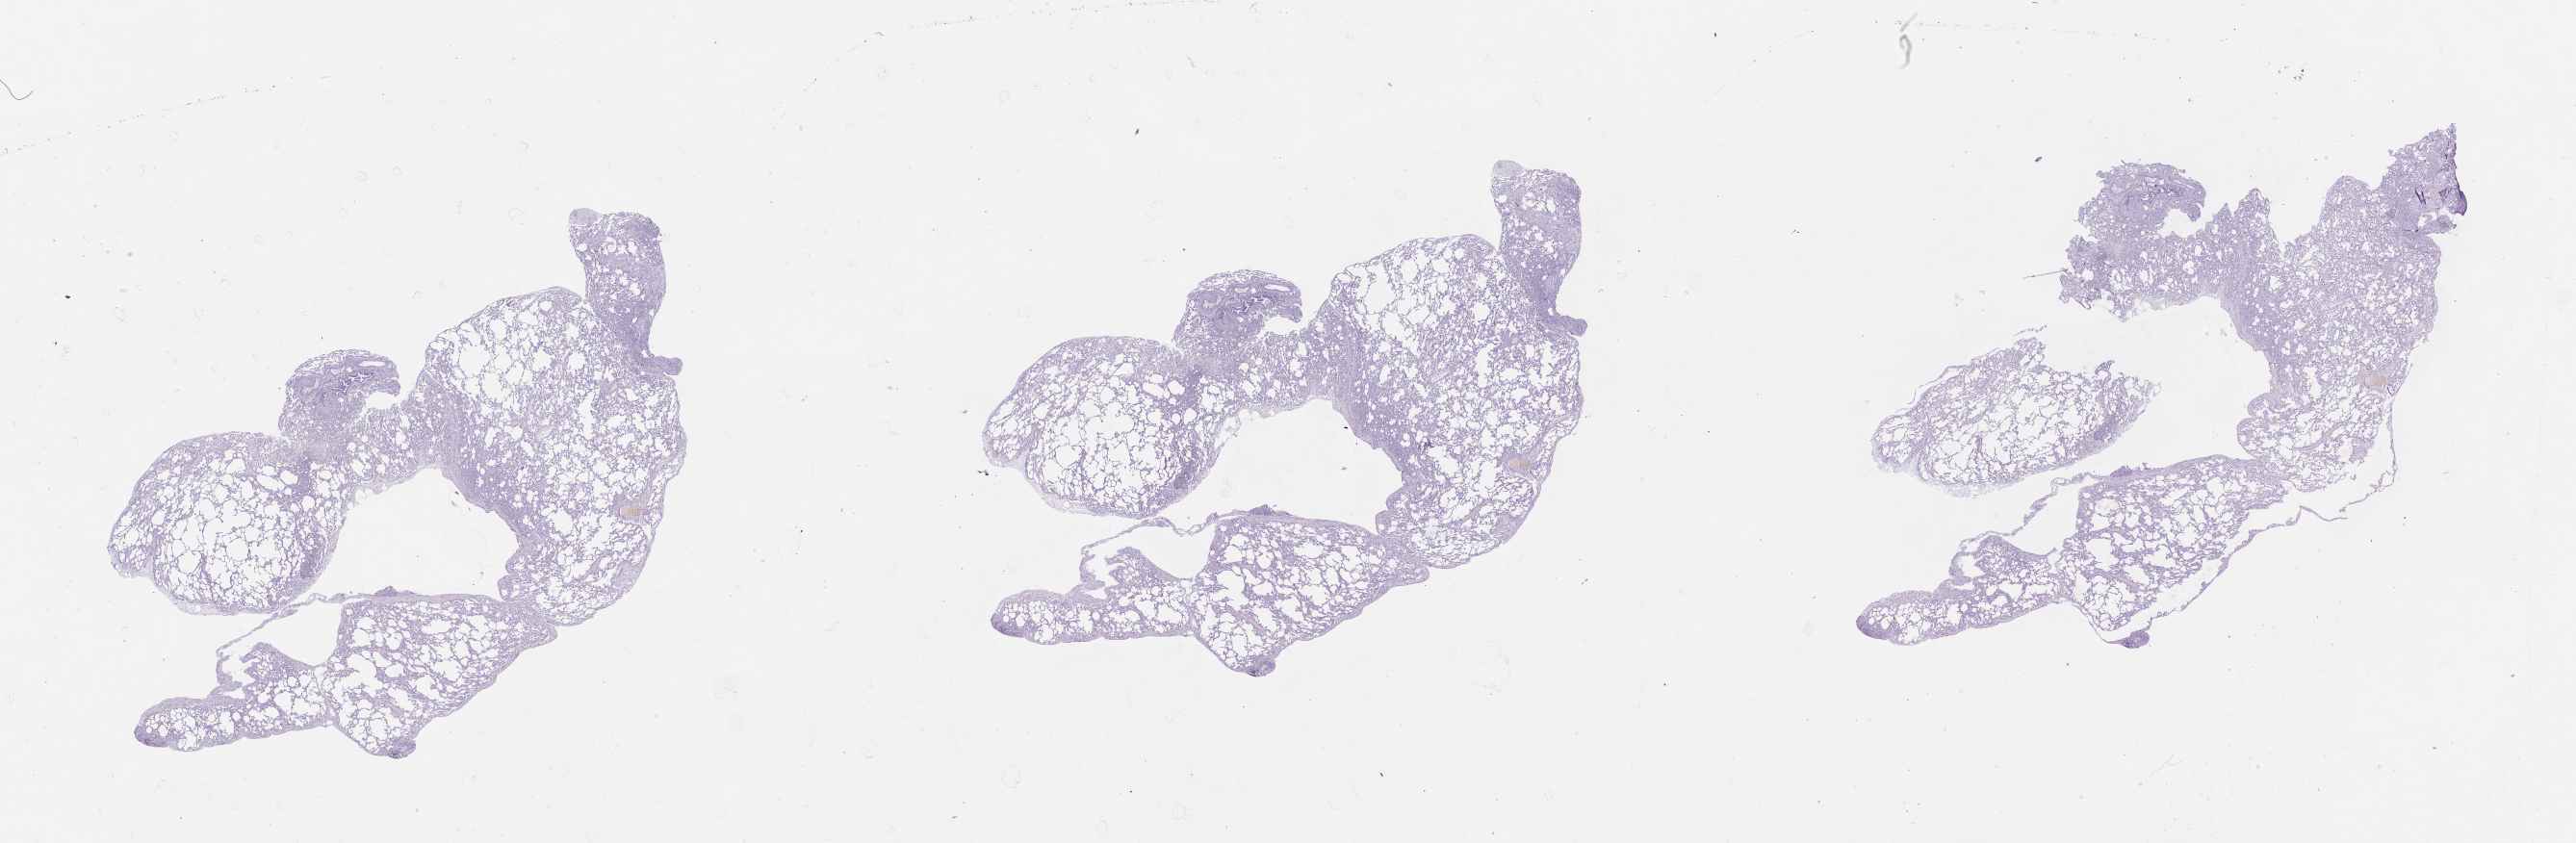
Whole-slide histology image, H&E — low-resolution overview of the scanned area, about 43.1 x 14.1 mm (slide scanned at 20x); lung, tissue type not recorded.
Patient diagnosis (cohort enrolment): lung adenocarcinoma (lung).